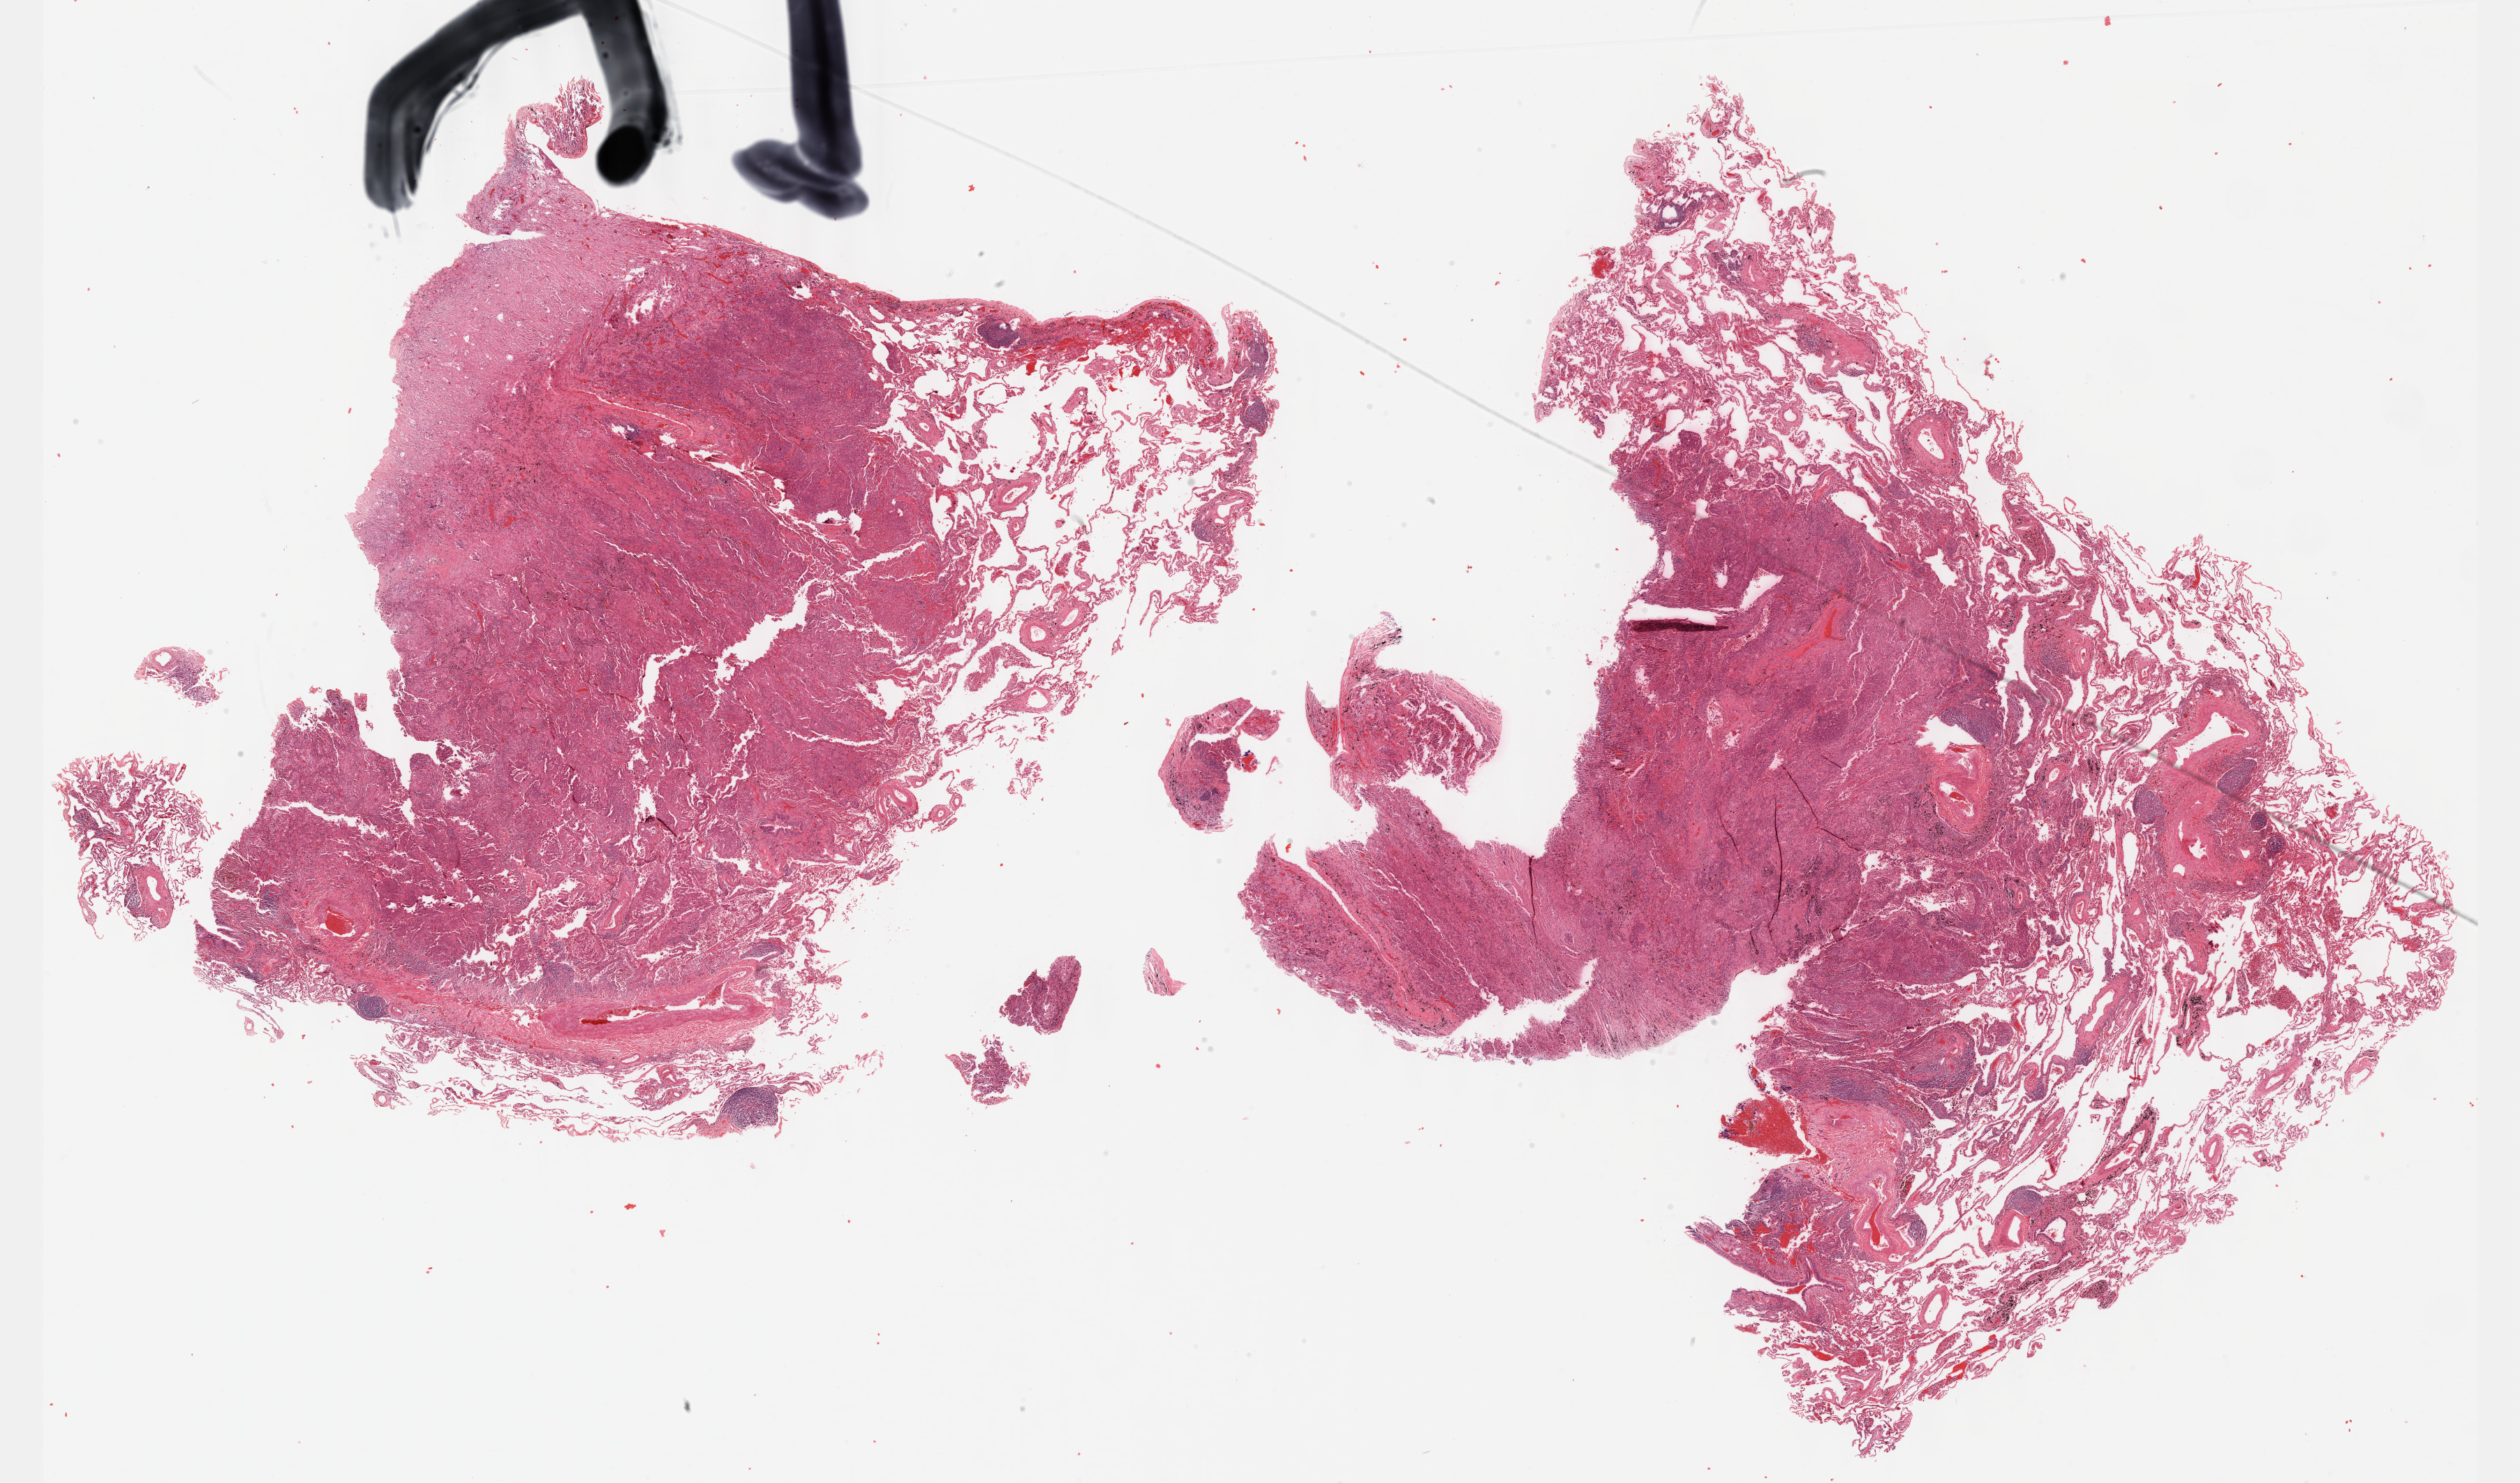
Digitized H&E tissue section (whole slide) — whole scanned area (about 29.2 x 17.2 mm, from a 40x scan) shown as a low-resolution overview; FFPE section; lung, primary tumour sample. Female patient; age at initial diagnosis 57 years.
- histologic diagnosis: Adenocarcinoma, NOS (lower lobe, lung)